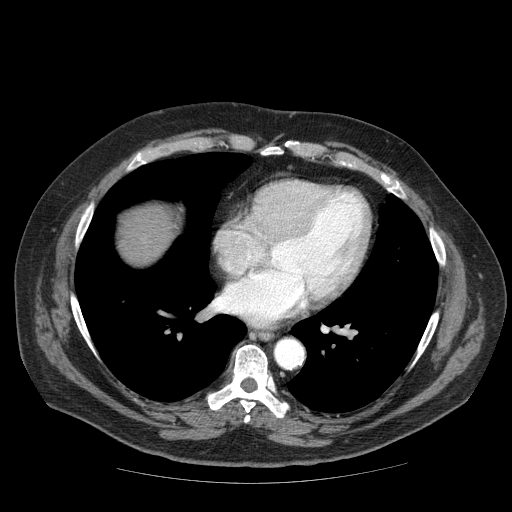
Contrast-enhanced abdominal CT (liver protocol), one axial slice; position 74 of 85 along the scan axis; soft-tissue window (W 400 / L 40 HU); 2.5 mm slice thickness; 512 × 512 image matrix. From the clinical record (not read from this slice): diagnosis: hepatocellular carcinoma (patient treated with transarterial chemoembolisation; whether this scan precedes or follows treatment is not stated here); TNM stage (as recorded): Stage-IIIA; Child-Pugh class: A.
Structures marked on this image (semi-automatically segmented with operator editing):
- liver parenchyma outside the tumour (the mass and vessels are separate outlines, so this box may not span the whole liver): bounding box (x1, y1, x2, y2) in pixels: (118, 206, 174, 264)